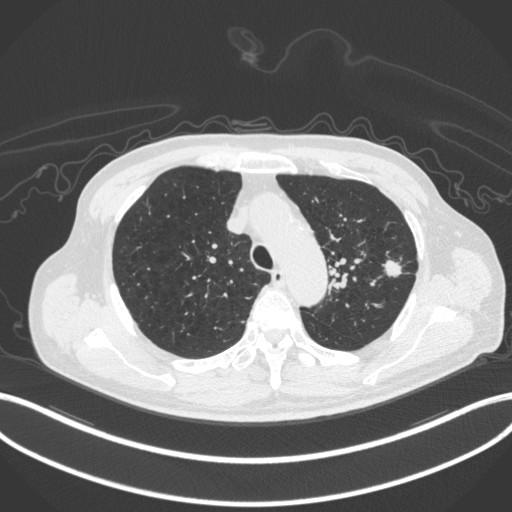
Chest CT, one axial slice. Position 335 of 420 along the scan axis. Reconstruction kernel B31f. 120 kVp. Lung window (W 1500 / L -600 HU). 1 mm slice thickness. 512 × 512 image matrix, field of view 400 × 400 mm. Patient: male, 77 years. From the clinical record (not read from this slice): clinical TNM (as recorded): T3 N1 M0.
Structures marked on this image (bounding box drawn by a radiologist):
- lung tumour (recorded histology: adenocarcinoma): bounding box <377,255,405,282> (left, top, right, bottom; pixels)